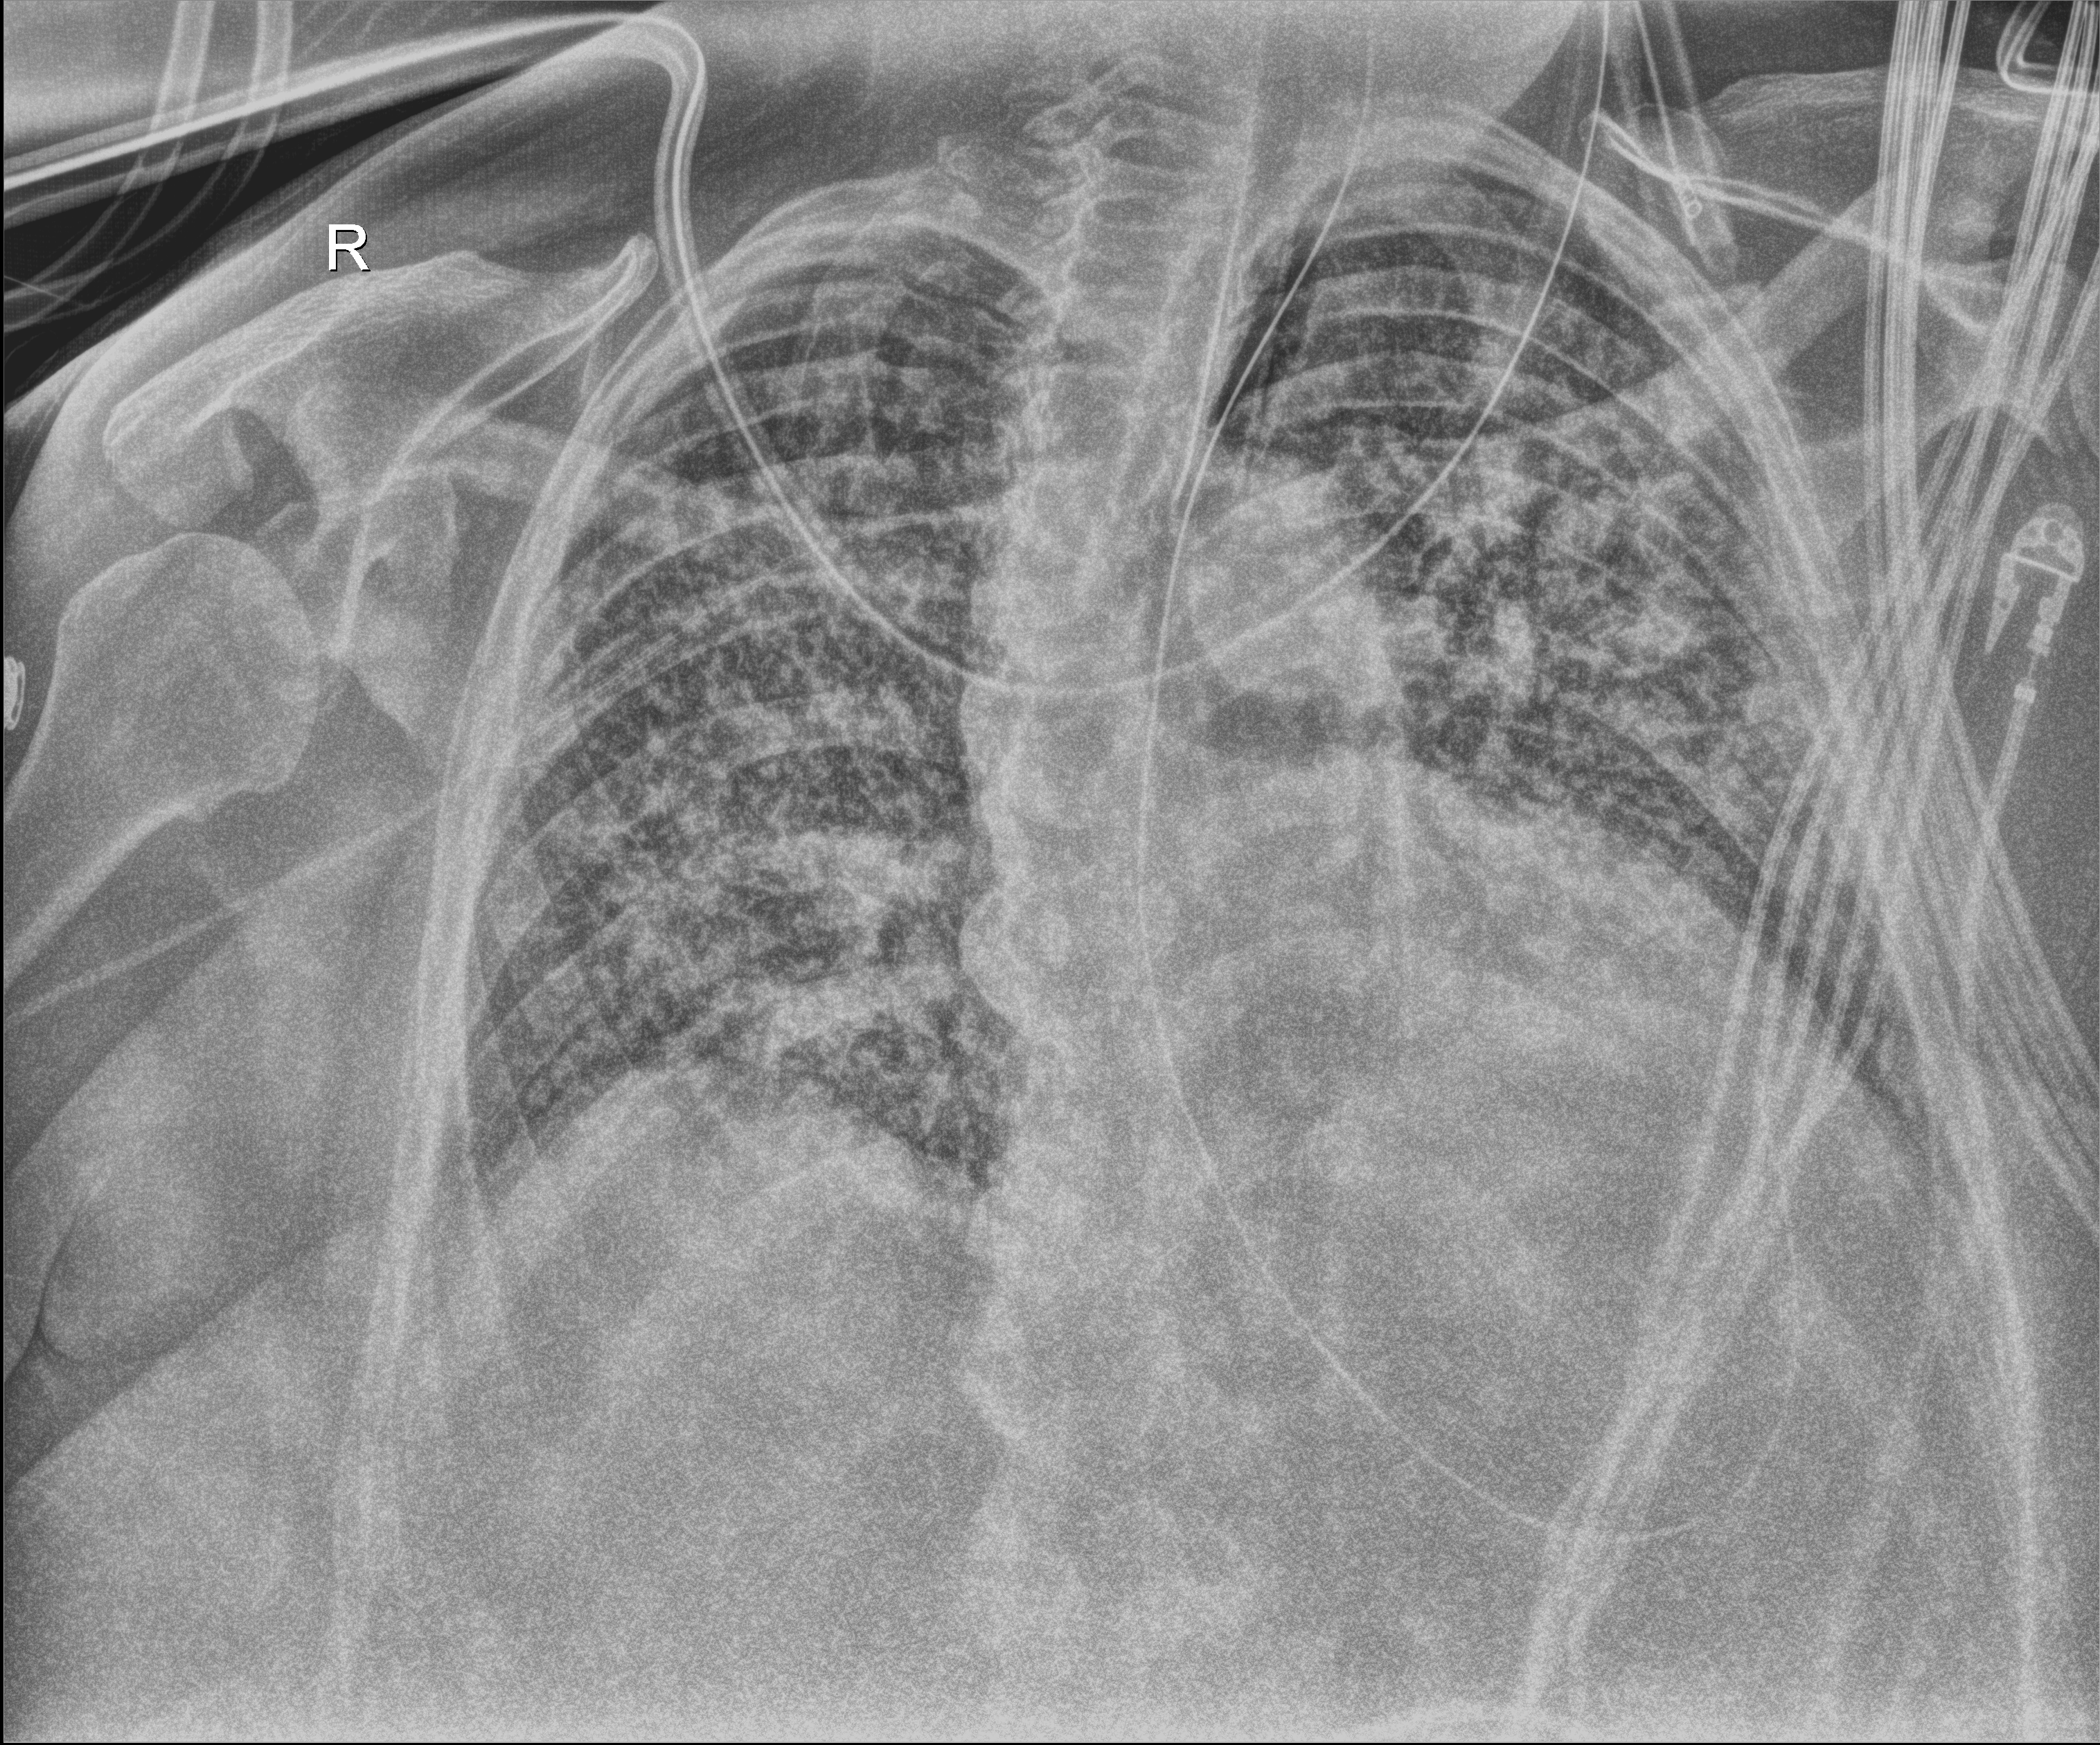
Chest radiograph. Adult patient hospitalised with COVID-19, age 18–59 years.
Admission-level facts for this patient (not findings on this image; timing relative to this image not recorded): admitted to intensive care during this hospital stay: yes; mechanically ventilated during this hospital stay: yes.